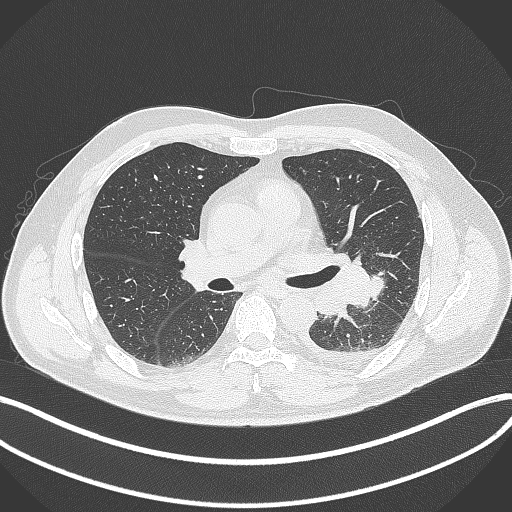
Chest CT, one axial slice; slice 205 of 342 in the series (ordered by position); reconstruction kernel B70f; 120 kVp; lung window (W 1500 / L -600 HU); 1 mm slice thickness; 512 × 512 image matrix, field of view 400 × 400 mm. Patient: male, 58 years. Case-level facts recorded for this patient, not image findings: clinical TNM (as recorded): T3 N1 M1b; histopathological grade: G3.
Structures marked on this image (bounding box drawn by a radiologist):
- lung tumour (recorded histology: small cell carcinoma): bounding box <345,253,381,308> (left, top, right, bottom; pixels)